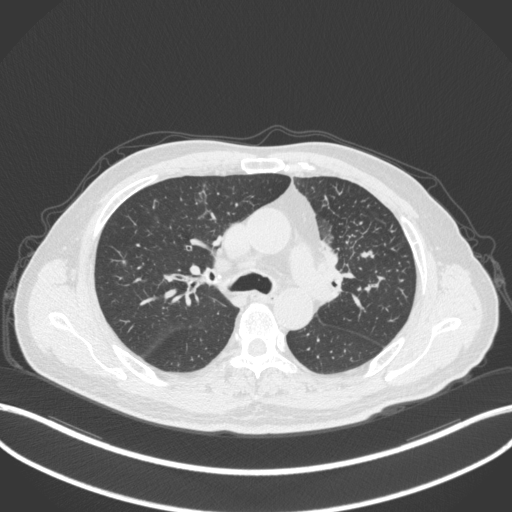
Chest CT, one axial slice. Slice 225 of 386 in the series (ordered by position). 120 kVp. Lung window (W 1500 / L -600 HU). 1 mm slice thickness. 512 × 512 image matrix. Patient: male, 69 years. From the clinical record (not read from this slice): clinical TNM (as recorded): T2a N2 M0.
Outlined on this slice (rectangle marked by the reading radiologist):
- lung tumour (recorded histology: adenocarcinoma): bounding box [x1, y1, x2, y2] px = [319, 243, 349, 290]